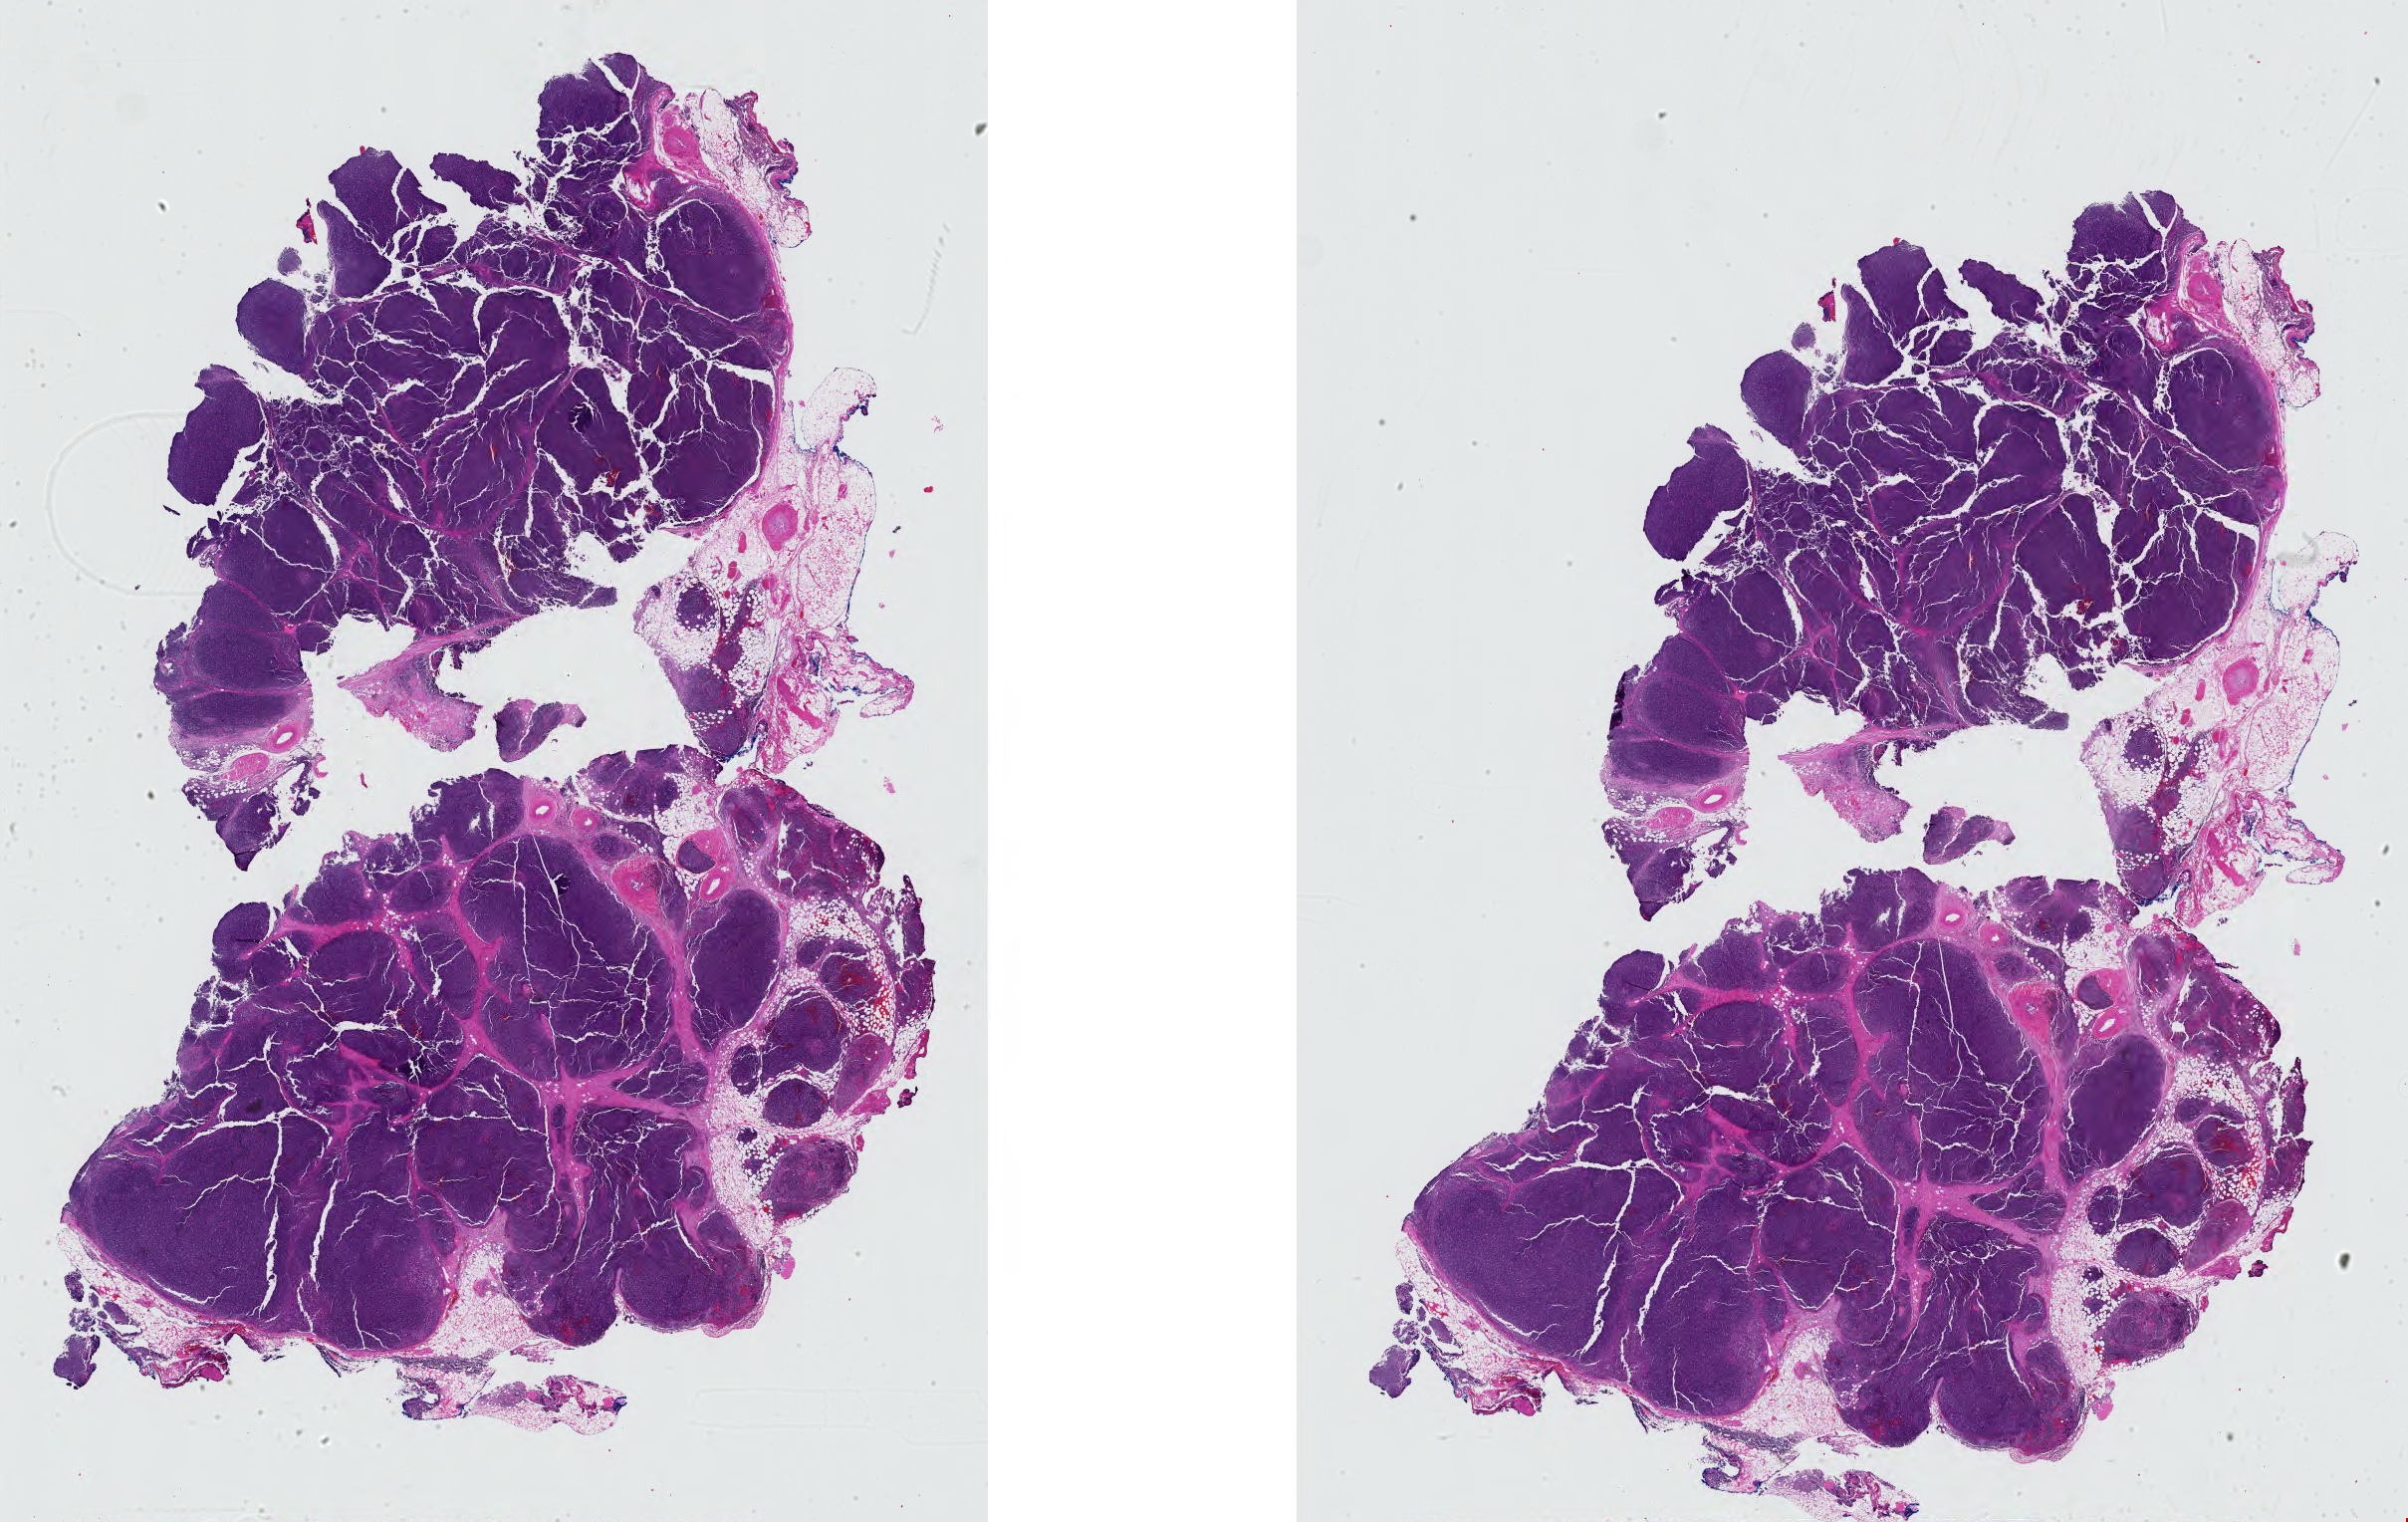
Hematoxylin and eosin (H&E) stained whole-slide image — low-resolution overview of the scanned area, about 35.1 x 22.1 mm (acquisition: 40x scan); formalin-fixed paraffin-embedded (FFPE) diagnostic section; sample: primary tumour, thymus. Female patient; age at initial diagnosis 31 years.
Histologic diagnosis: Thymoma, type B1, malignant.